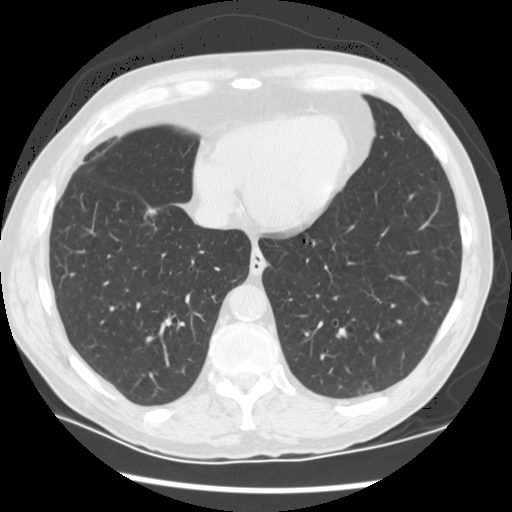
Chest CT (low-dose screening protocol), one axial image; first (baseline) screen; lung window (W 1500 / L -600 HU); 120 kVp; slice 92 of 122 in the series; 512 × 512 image matrix, field of view 360 × 360 mm. Male participant, aged 68 years at enrolment. Current smoker at enrolment.
- Expert reader's lesion annotation, box from (x=123, y=185) to (x=189, y=238) px.
- The screening reader recorded 3 non-calcified nodules or masses ≥4 mm on this exam (right upper lobe, right upper lobe, right lower lobe); which of them this box marks is not recorded.
- Participant outcome: lung cancer diagnosed 90 days after this screen — adenocarcinoma, NOS, right upper lobe, right lower lobe, well differentiated (G1), stage IV (AJCC 6th edition), 35 mm at pathology.